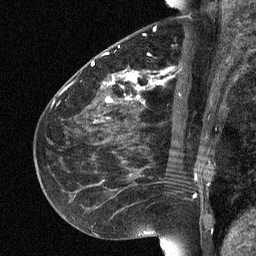
Breast MRI (dynamic contrast-enhanced), one sagittal slice. Slice 27 of 64 in the series (ordered by position). Dynamic contrast-enhanced study with each time point stored as its own series, time point 2 of 3 at this slice position (early post-contrast, ordered by acquisition time). 1.5 T. TE 4.8 ms, TR 27 ms. 256 × 256 image matrix, field of view 180 × 180 mm. Female patient, age 51 years. Case-level facts recorded for this patient, not image findings: setting: breast cancer imaged before/during neoadjuvant chemotherapy; receptor status: HR-positive, HER2-negative.
Structures marked on this image (semi-automatically segmented with operator editing):
- analysis volume of interest (the breast-tissue region the enhancement analysis was run in; not a lesion): bounding box [x1, y1, x2, y2] px = [72, 34, 182, 118]
- tumour enhancement mask (voxels above the 90 % enhancement threshold inside the analysis volume of interest): [92, 62, 141, 102]